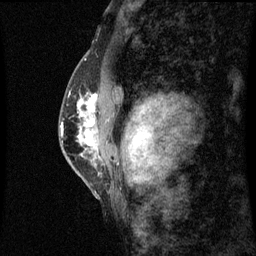
Breast MRI (dynamic contrast-enhanced), one sagittal slice; slice 39 of 60 in the series (ordered by position); dynamic contrast-enhanced series, image 2 of 3 at this slice position (ordered by acquisition); 1.5 T; TE 4.2 ms, TR 8.9 ms; 2 mm slice thickness; 256 × 256 image matrix, field of view 200 × 200 mm. Female patient, age 50 years. From the clinical record (not read from this slice): setting: breast cancer imaged before/during neoadjuvant chemotherapy; receptor status: triple-negative.
Annotated regions visible in this slice (semi-automatically segmented with operator editing):
- analysis volume of interest (the breast-tissue region the enhancement analysis was run in; not a lesion): bounding box <68,80,100,169> (left, top, right, bottom; pixels)
- tumour enhancement mask (voxels above the 70 % enhancement threshold inside the analysis volume of interest): <80,96,98,147>